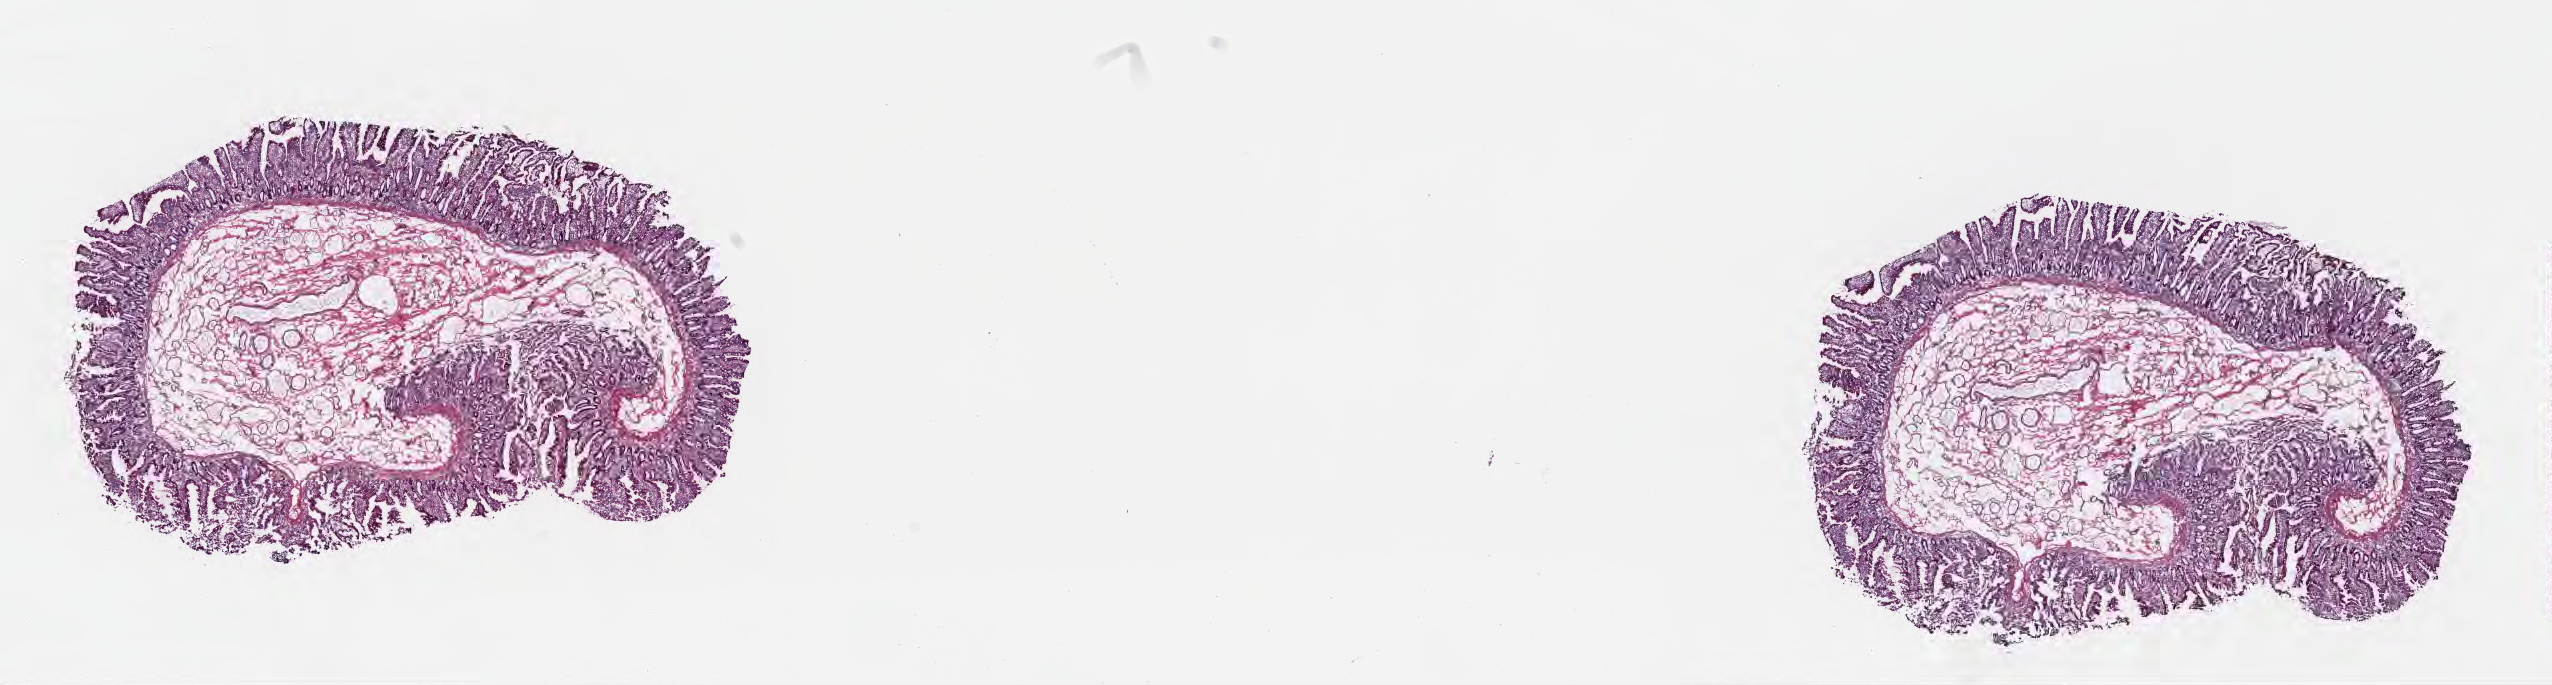
Hematoxylin and eosin (H&E) whole-slide image, low-resolution overview of the scanned area, about 20.6 x 5.5 mm; frozen section (tissue freezing medium); specimen: non-tumor (normal tissue) sample from a patient with infiltrating duct carcinoma, NOS; anatomic site: head of pancreas. Male patient; age at initial diagnosis 75 years. Slide review estimates, as recorded: tumor cells 0%, tumor nuclei 0%, stromal cells 45%, necrosis 0%, normal cells 55%. Infiltration values recorded for this section: lymphocyte infiltration 50%, monocyte infiltration 3%, neutrophil infiltration 0%.
This section: non-tumor tissue sample; the patient's diagnosis is given above. Section: top of the tissue portion.